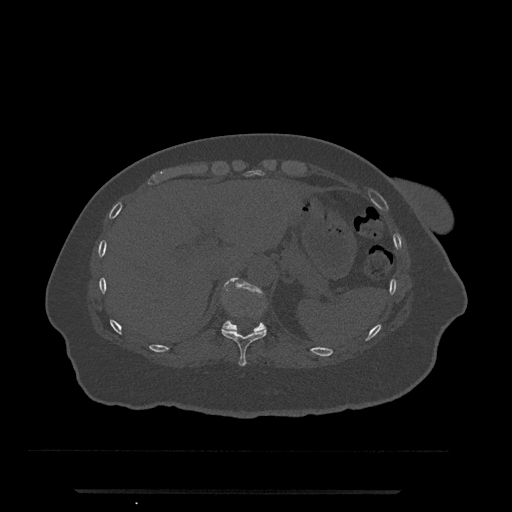
CT including the spine, one axial slice. Position 265 of 797 along the scan axis. Reconstruction kernel Br40s/3. 120 kVp. Bone window (W 1800 / L 400 HU). 0.5 mm slice thickness. 512 × 512 image matrix. Patient: female, 51 years. From the clinical record (not read from this slice): primary cancer: neuro.
Outlined on this slice (semi-automatic segmentation, software-assisted and operator-edited):
- T10 vertebra: bounding box [x1, y1, x2, y2] px = [221, 327, 267, 366]
- T11 vertebra: [223, 278, 265, 332]